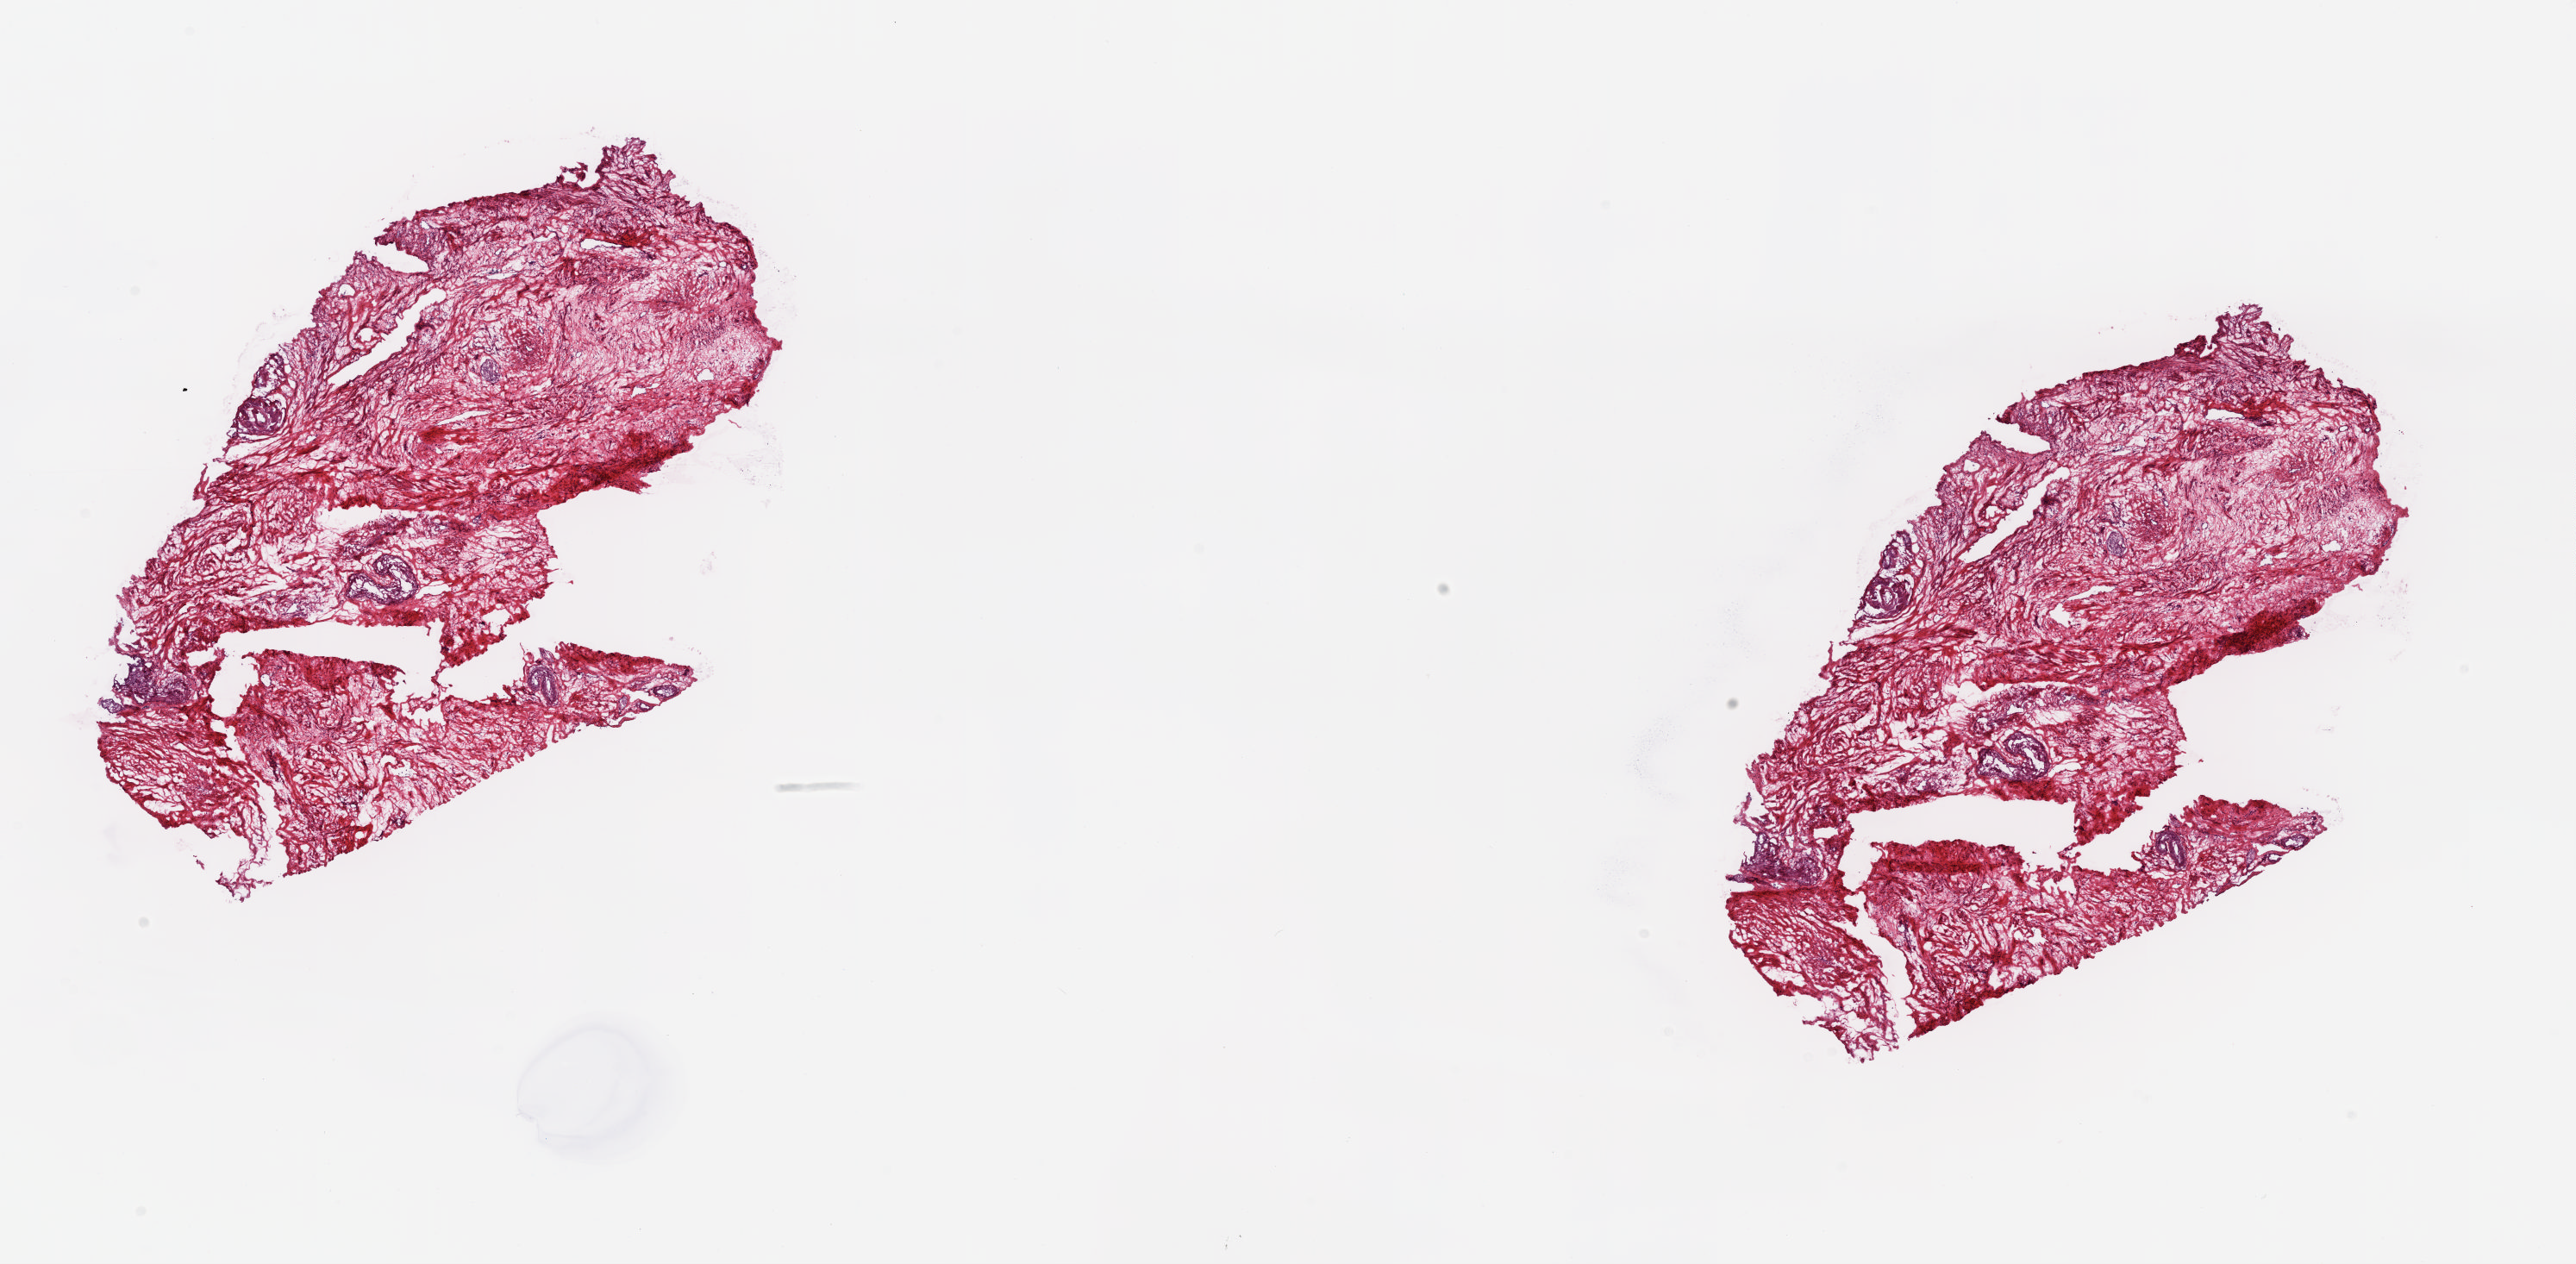
Hematoxylin and eosin (H&E) stained whole-slide image, a low-resolution overview of the entire scanned area, about 23.6 x 11.6 mm (slide scanned at 20x), frozen section, sample: solid tissue normal (non-tumour tissue), uterus. Female patient. Pathologist review of this section (percent, as recorded): tumour cells 0%, tumour nuclei 0%, normal cells 100%, stromal cells 0%, necrosis 0%. Infiltration values recorded for this section: lymphocyte infiltration 0%, monocyte infiltration 0%, neutrophil infiltration 0%.
- this section: solid tissue normal (non-tumour) sample from the same patient
- patient diagnosis: Endometrioid adenocarcinoma, NOS